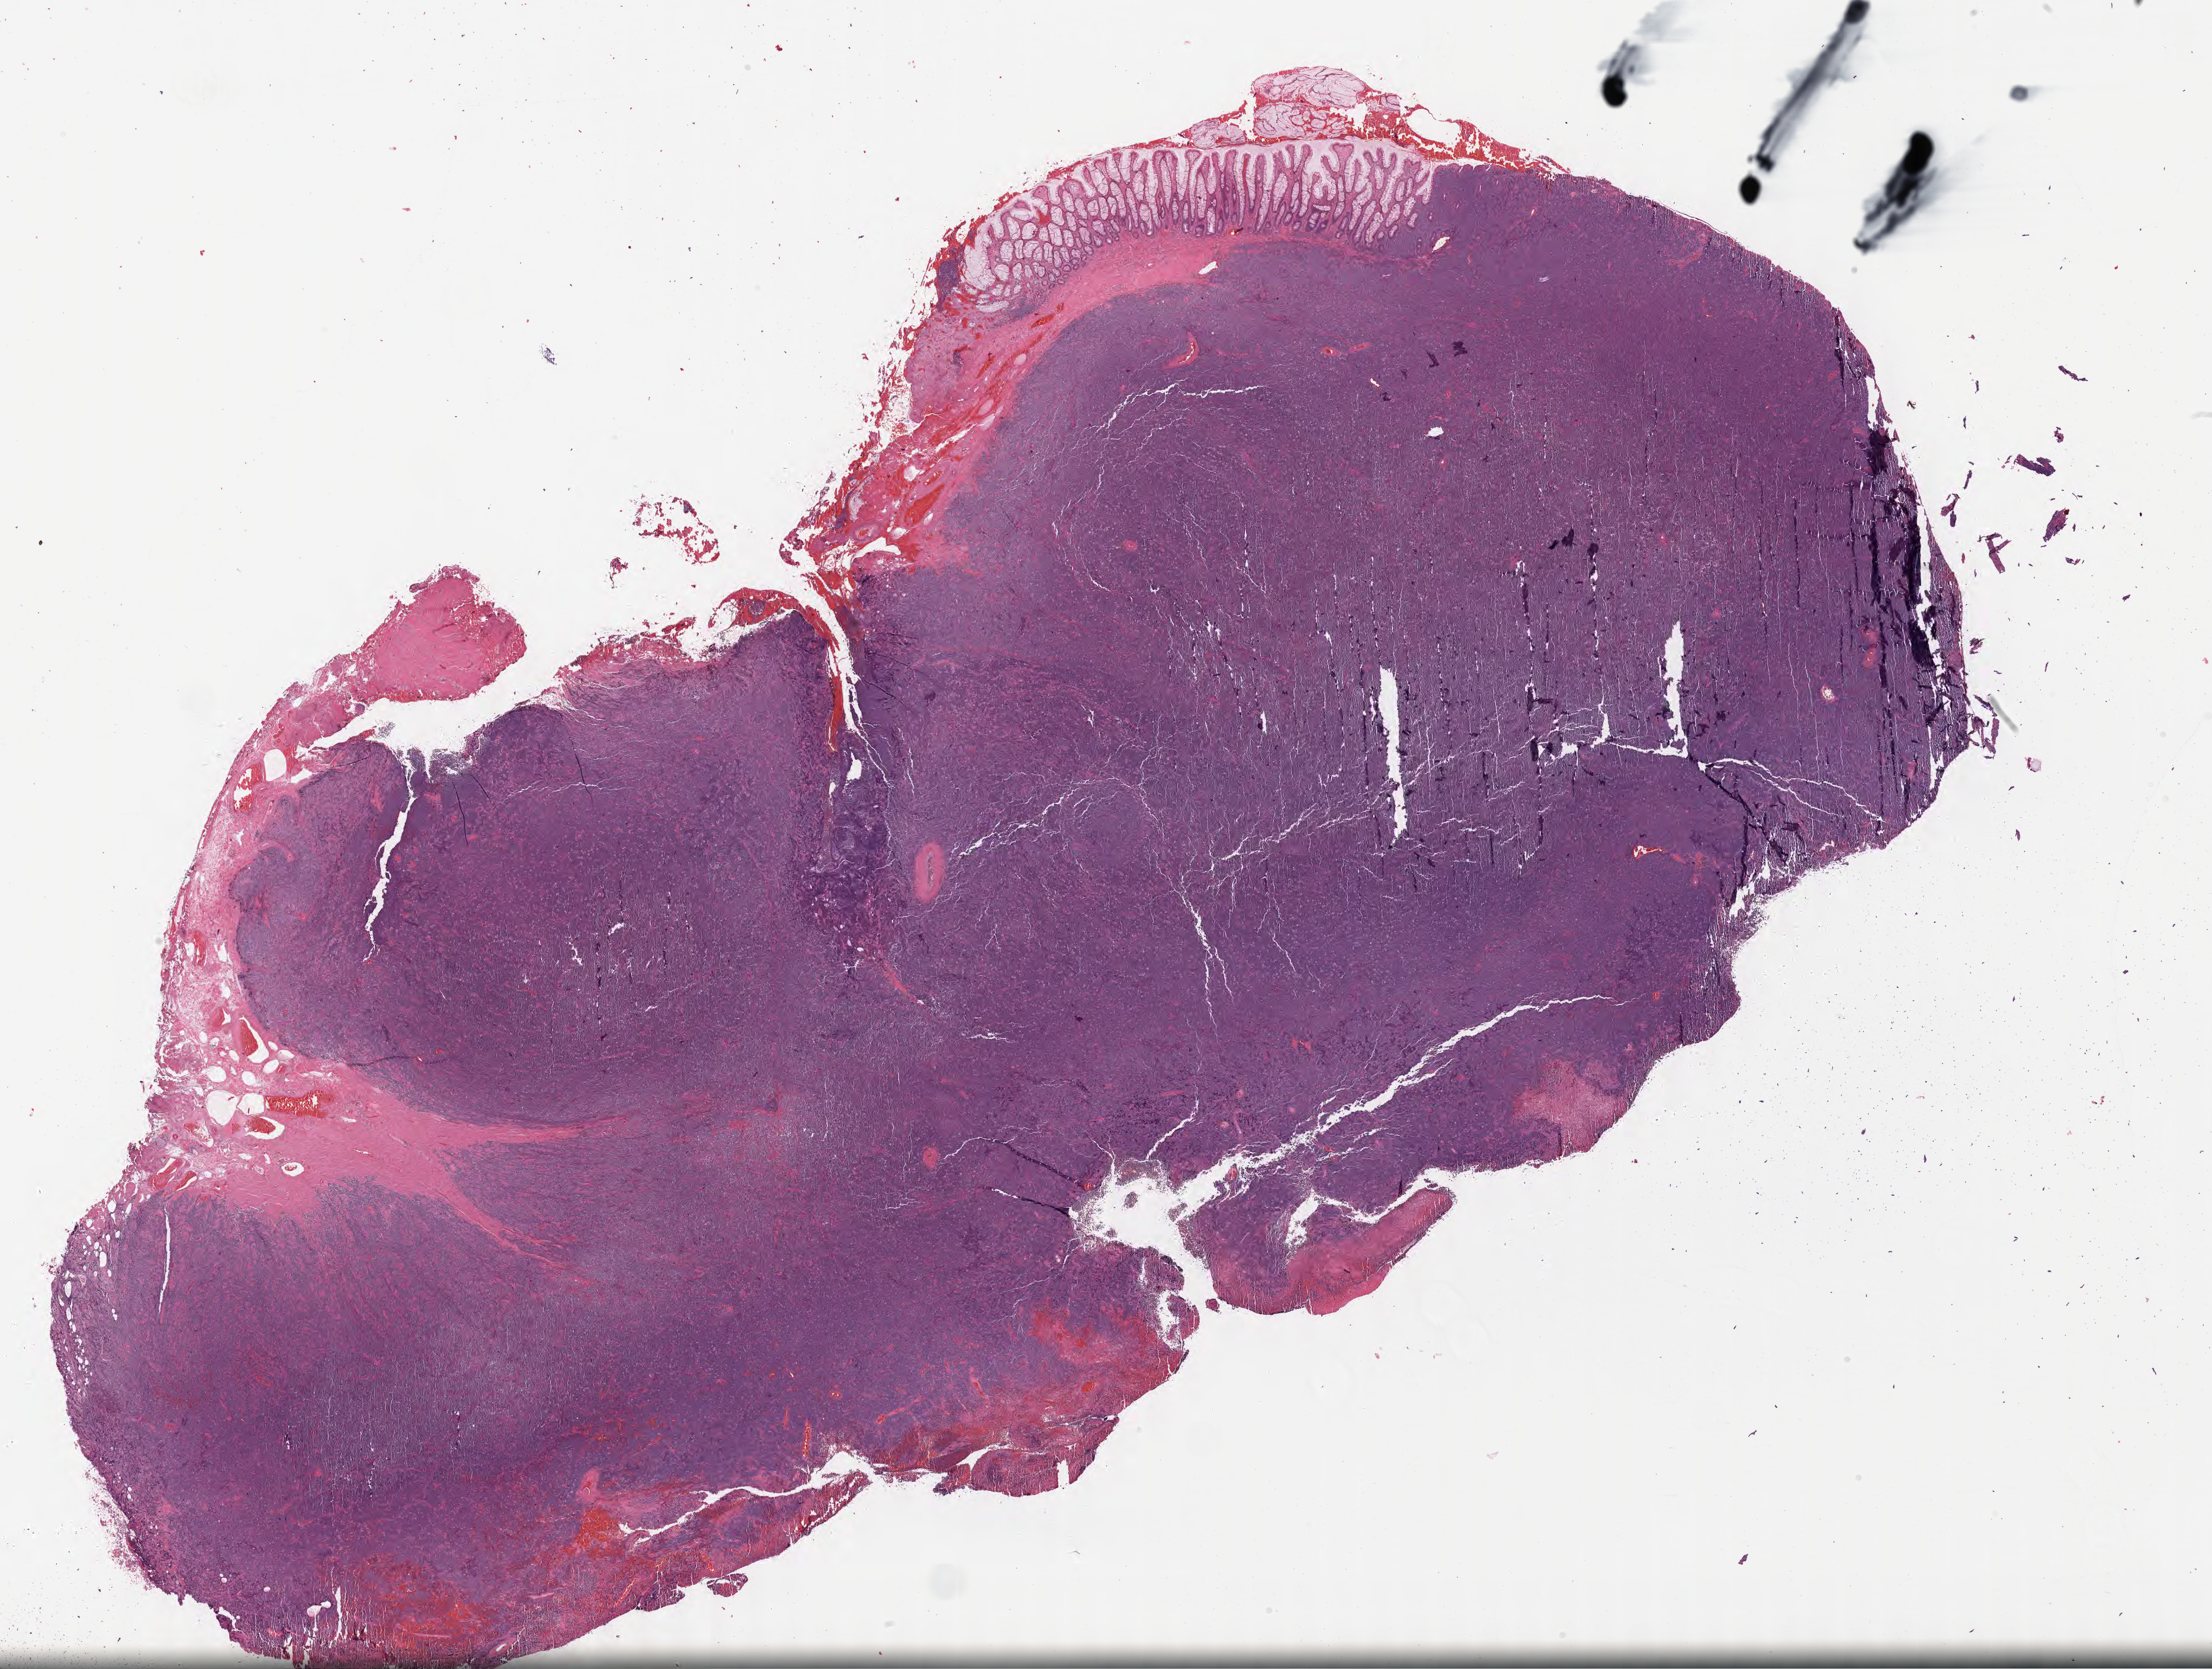
Hematoxylin and eosin (H&E) whole-slide image, shown as a low-resolution overview of the whole scanned area (about 30.2 x 22.8 mm), tumor tissue. Patient: female, 29 years old.
Histologic diagnosis: Burkitt lymphoma, NOS.